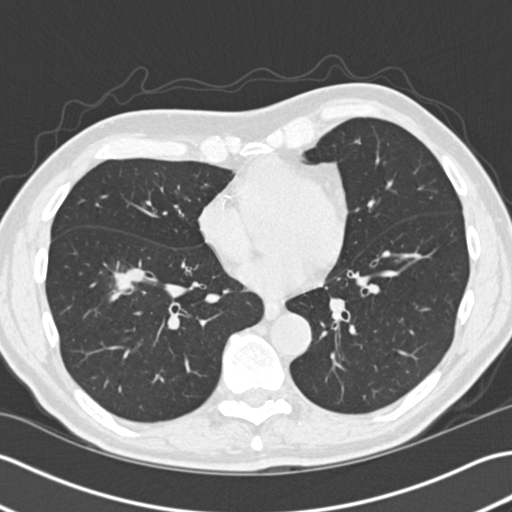
Axial slice from a low-dose chest CT screening exam. Second screening round (one year after baseline). Lung window (W 1500 / L -600 HU). 512 × 512 image matrix, field of view 350 × 350 mm. Male, age 73 years at enrolment. Former smoker at enrolment.
- Expert reader's lesion annotation, bounding box <93,250,152,315> (left, top, right, bottom; pixels).
- Screening reader's record for this exam (one nodule recorded; not confirmed to be the boxed lesion): non-calcified nodule or mass ≥4 mm, right lower lobe, 18 × 15 mm, spiculated (stellate) margins, soft tissue attenuation, pre-existing on the prior screen: yes.